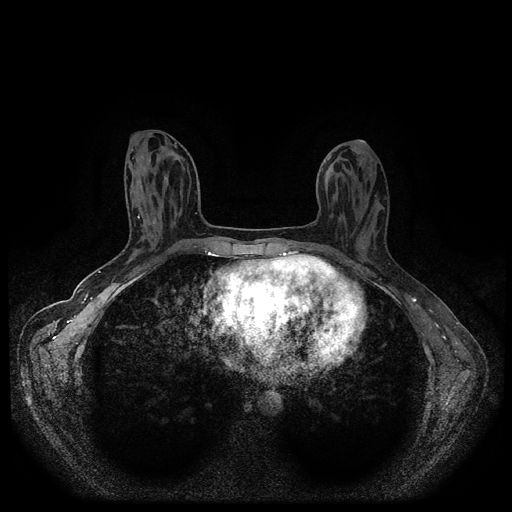
Breast MRI (dynamic contrast-enhanced, multi-phase), one axial slice; slice 41 of 116 in the series (ordered by position); dynamic contrast-enhanced series, time point 2 of 5 at this slice position (early post-contrast); 1.5 T; TE 2.6 ms, TR 5.4 ms; 512 × 512 image matrix, field of view 340 × 340 mm. Female patient, age 30 years.
Outlined on this slice (semi-automatic segmentation, software-assisted and operator-edited):
- breast lesion (labelled benign in the annotation): box from (x=353, y=235) to (x=370, y=251) px